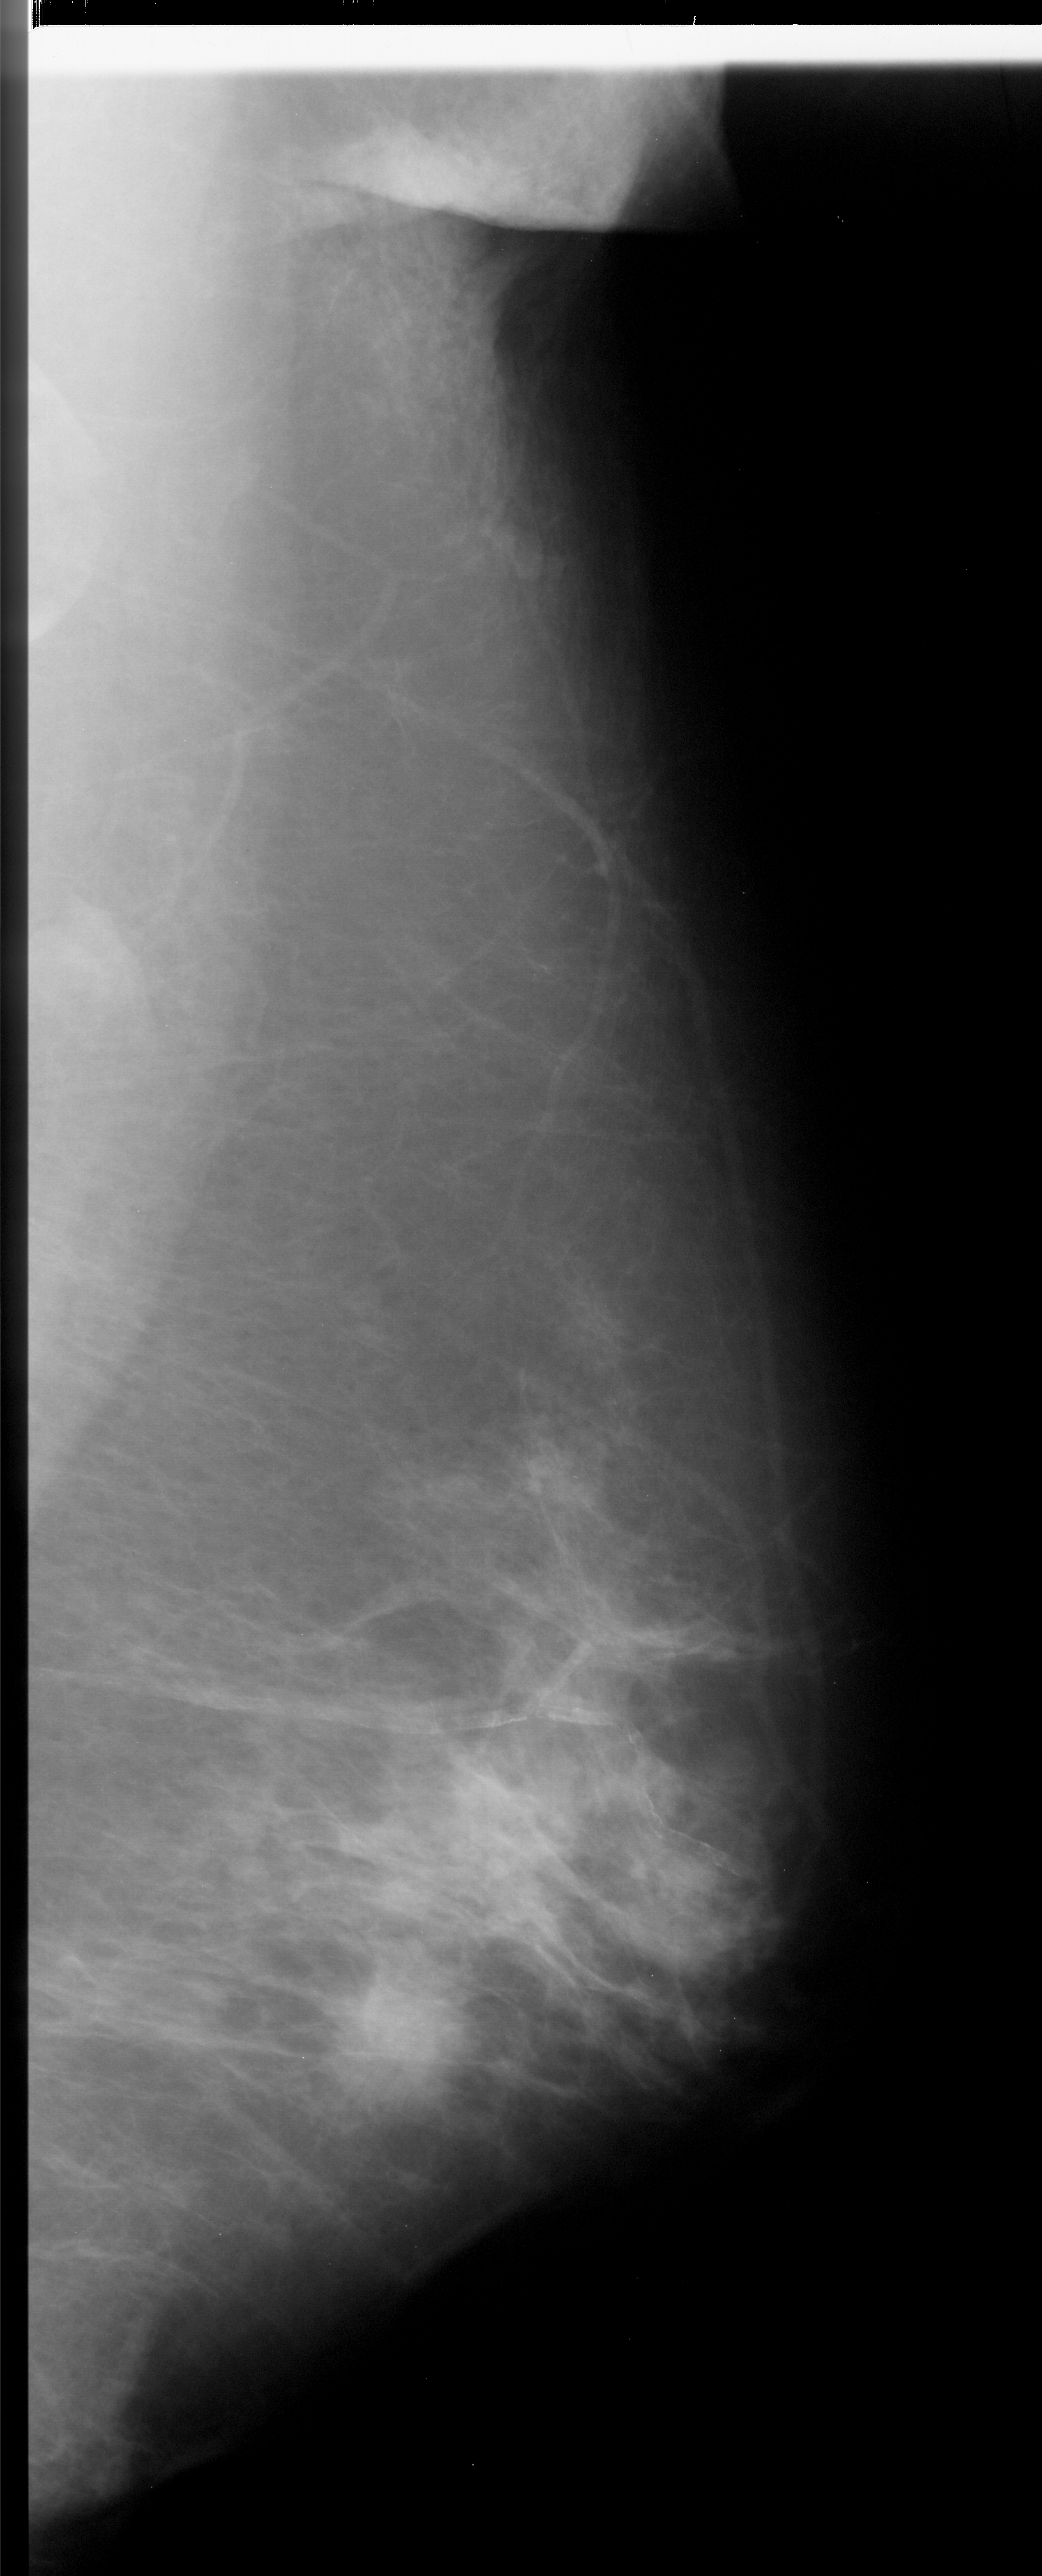
Mammogram (digitized film); right breast; MLO view; breast composition: scattered fibroglandular densities (BI-RADS density category 2 of 4); 1042 × 2576 image matrix.
Marked abnormalities (boxes around the expert regions of interest):
- mass, shape irregular, margins spiculated; BI-RADS assessment category 5; pathology result (as recorded, not read from the image): malignant: bounding box (x1, y1, x2, y2) in pixels: (327, 1960, 487, 2102)